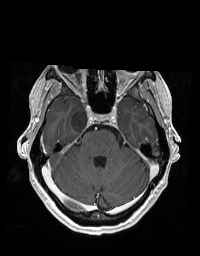
Brain MRI from a brain-tumour surgery series, one axial slice. Position 129 of 192 along the scan axis. T1-weighted post-contrast. 1 mm slice thickness. 200 × 256 image matrix, field of view 195 × 250 mm. Case-level facts recorded for this patient, not image findings: histopathology: Glioblastoma; WHO grade: 2; IDH mutation: no; tumour location: Right Skull Base Temporal.
Annotated regions visible in this slice (outlined manually by an expert reader):
- tumour: bounding box [x1, y1, x2, y2] px = [71, 109, 87, 132]